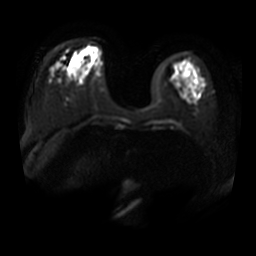
Breast MRI, one axial slice. Slice 10 of 34 in the series (ordered by position). Diffusion-weighted series; image 2 of 4 stored at this slice position (different b-values; order by instance number). 3 T. 5 mm slice thickness. 256 × 256 image matrix, field of view 380 × 380 mm. Female patient.
Annotated regions visible in this slice (outlined manually by an expert reader):
- tumour on diffusion-weighted imaging: bounding box [x1, y1, x2, y2] px = [80, 48, 89, 59]